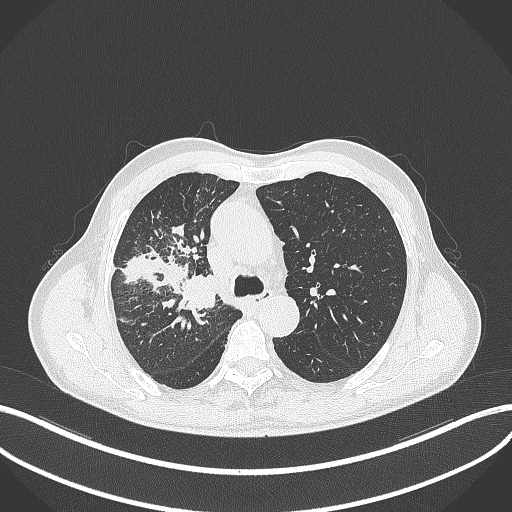
Chest CT, one axial slice; slice 332 of 490 in the series (ordered by position); reconstruction kernel B70f; 120 kVp; lung window (W 1500 / L -600 HU); 1 mm slice thickness; 512 × 512 image matrix. Male patient, age 69 years. From the clinical record (not read from this slice): clinical TNM (as recorded): T2a N0 M0.
Structures marked on this image (rectangle marked by the reading radiologist):
- lung tumour (recorded histology: adenocarcinoma): bounding box (x1, y1, x2, y2) in pixels: (180, 273, 222, 314)